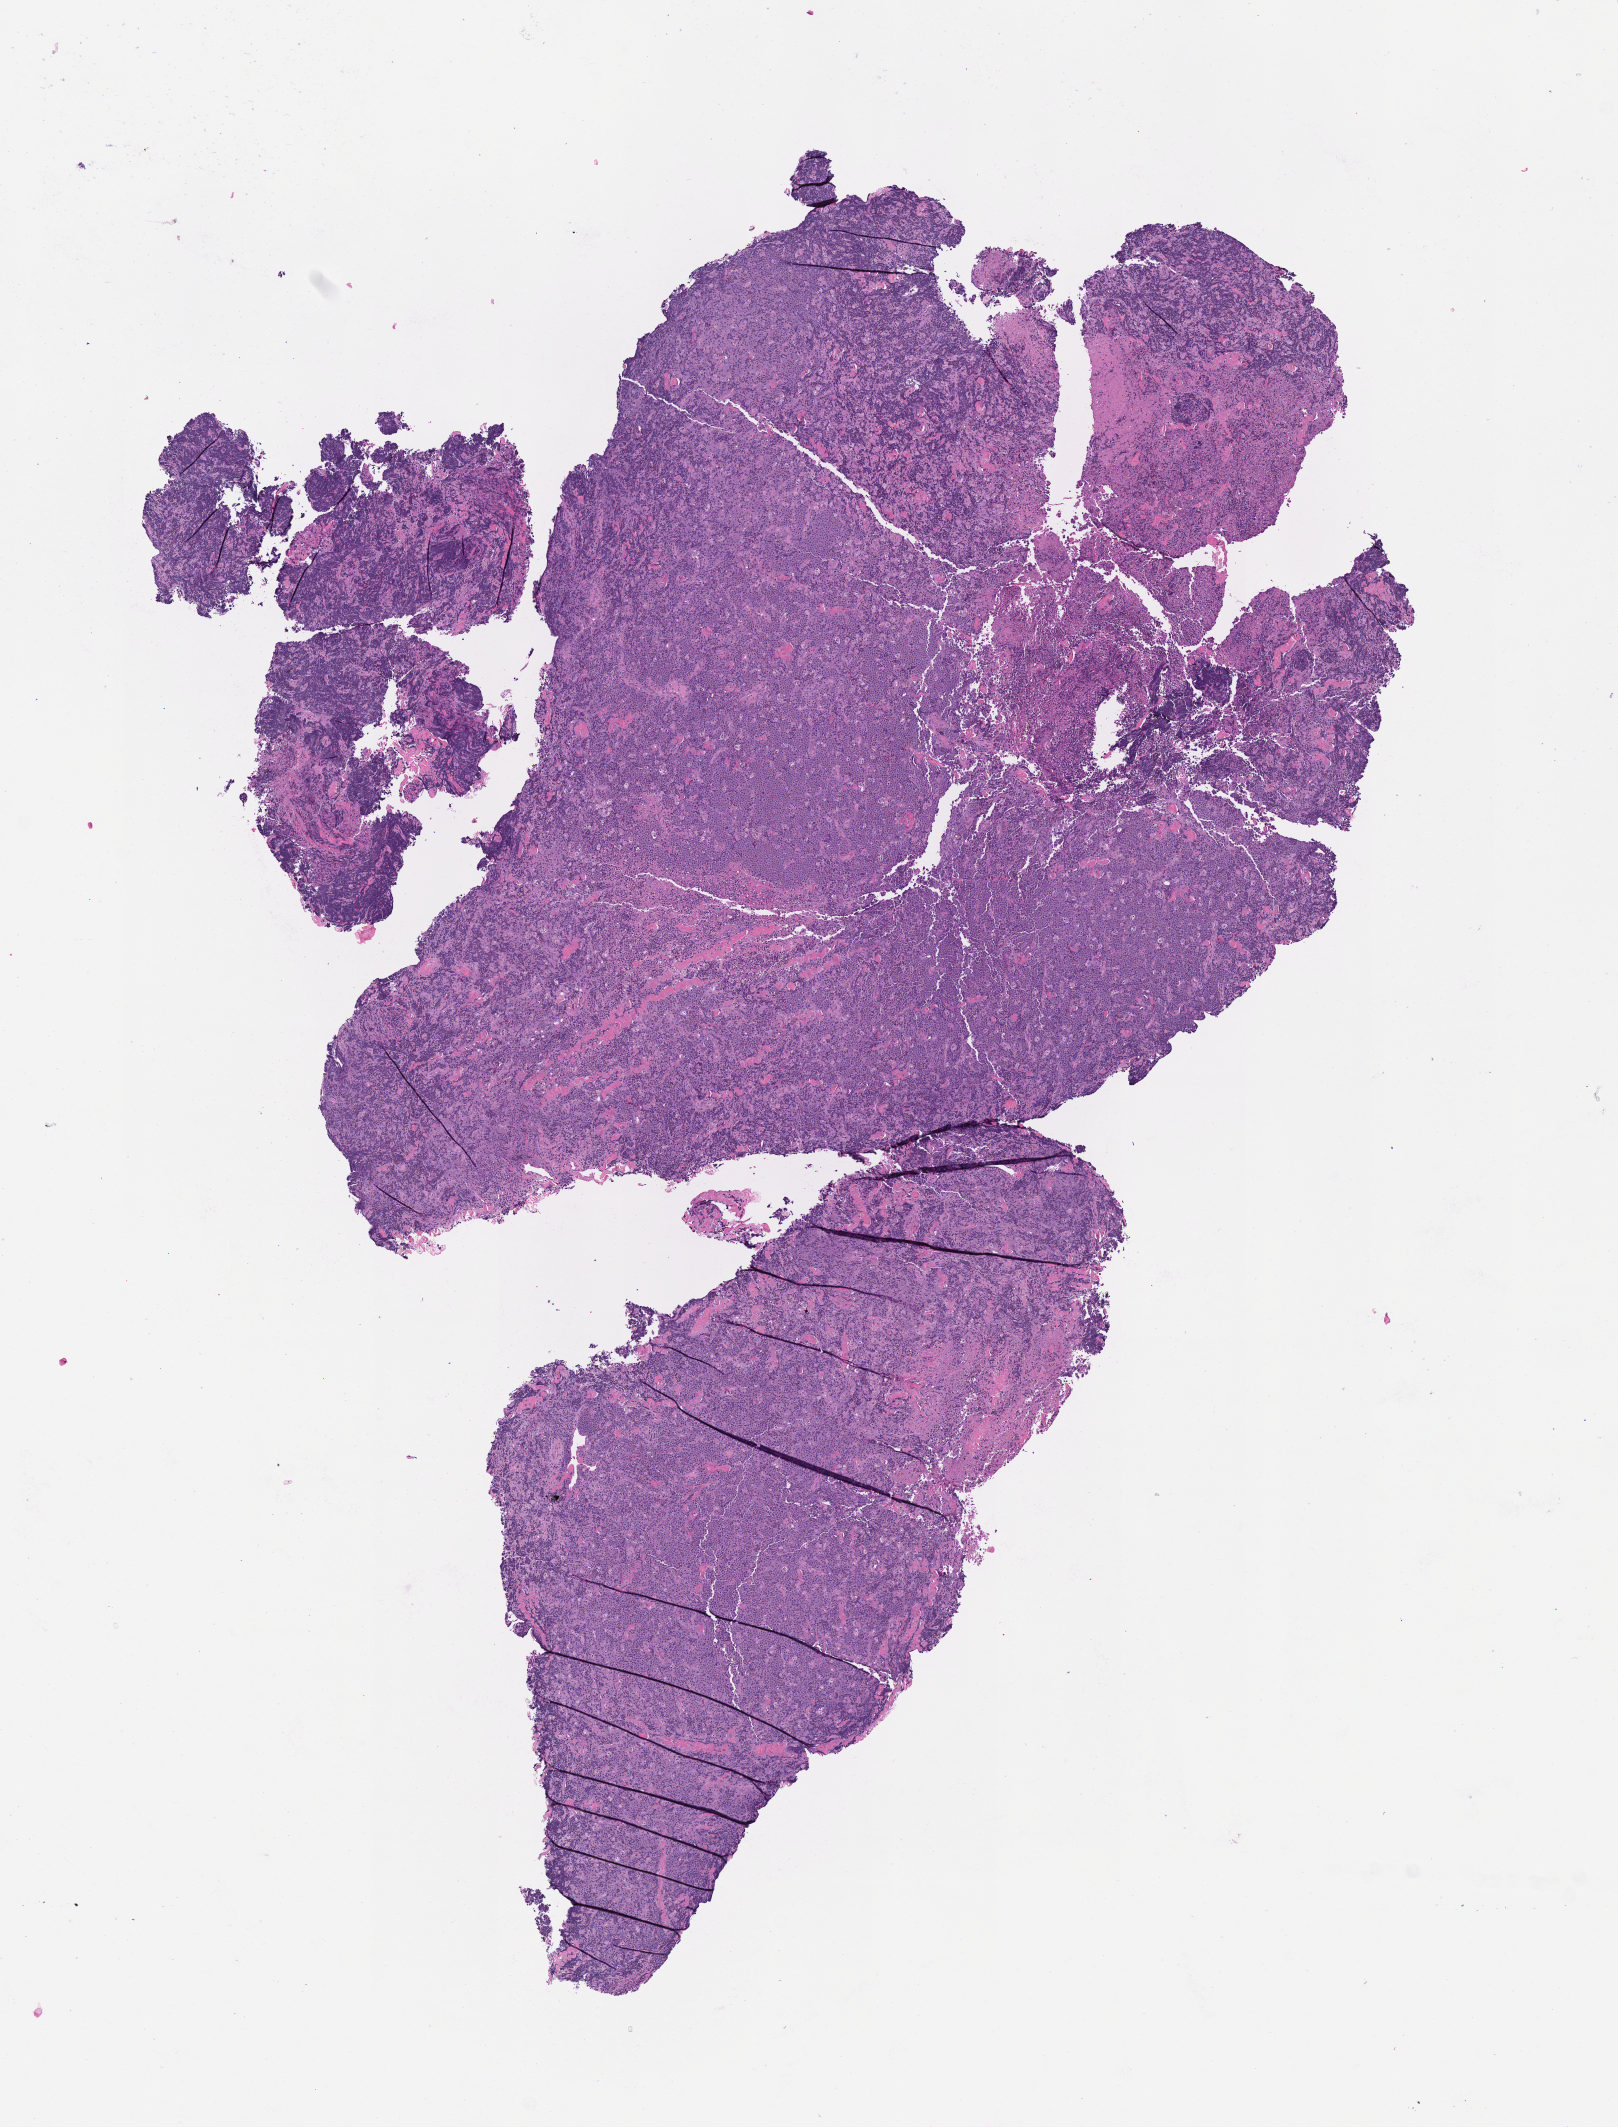
Digitized haematoxylin and eosin-stained section — whole scanned area (about 6.5 x 8.6 mm) shown as a low-resolution overview, formalin-fixed, paraffin-embedded (FFPE) tissue, specimen: primary tumor, anatomic site: mandible. Male patient, 25 years old. Composition of this section per pathologist review: tumor cells 90%, tumor nuclei 95%, stromal cells 5%, necrosis 5%, normal cells 0%. Inflammatory infiltration, as recorded: lymphocyte infiltration 15%, monocyte infiltration 30%, neutrophil infiltration 10%.
• Ann Arbor stage (patient): Stage IV
• diagnosis: Diffuse large B-cell lymphoma, NOS